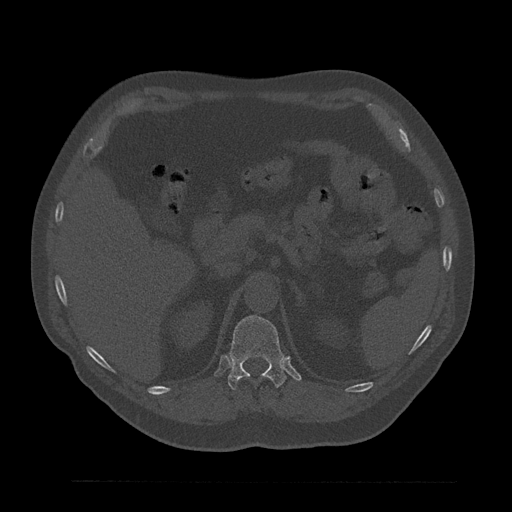
CT including the spine, one axial slice. Position 242 of 797 along the scan axis. Reconstruction kernel Br40s/3. 120 kVp. Bone window (W 1800 / L 400 HU). 0.5 mm slice thickness. 512 × 512 image matrix. Patient: male, 61 years. From the clinical record (not read from this slice): primary cancer: prostate.
Outlined on this slice (semi-automatically segmented with operator editing):
- T12 vertebra: bounding box <228,316,287,390> (left, top, right, bottom; pixels)